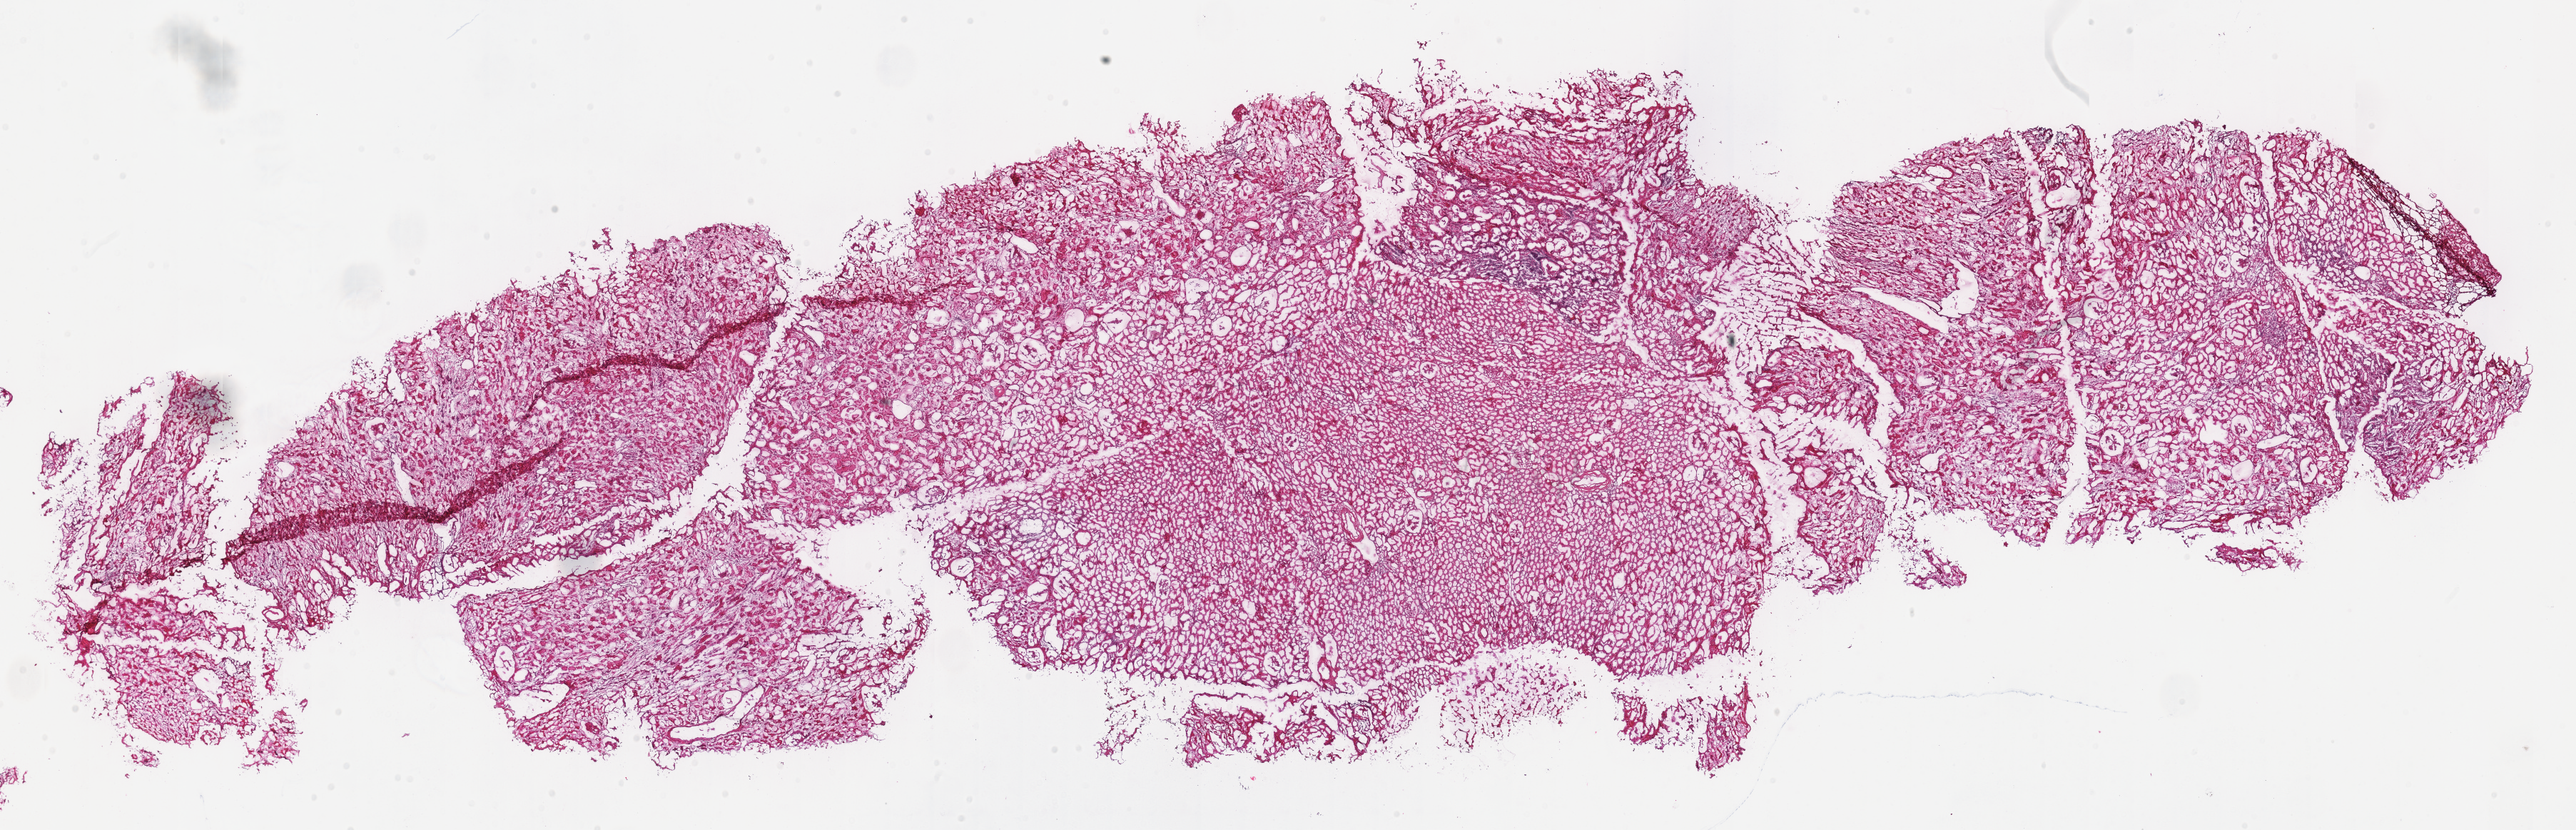
Whole-slide histology image, H&E-stained — a low-resolution overview of the entire scanned area, about 28.4 x 9.1 mm (from a 40x scan). Frozen section from the top of the tissue portion. Kidney, solid tissue normal (non-tumour tissue) sample. Patient: male, age at initial diagnosis 42 years.
This section: solid tissue normal sample (biorepository sample class). Patient diagnosis: Renal cell carcinoma, chromophobe type.